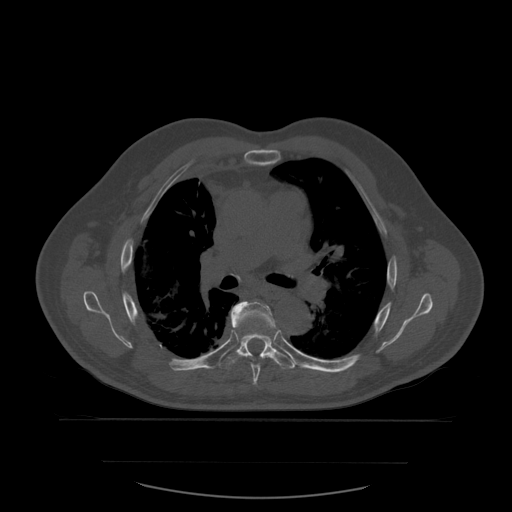
CT including the spine, one axial slice; slice 394 of 590 in the series (ordered by position); bone window (W 1800 / L 400 HU); 1.25 mm slice thickness; 512 × 512 image matrix, field of view 479 × 479 mm. Patient age 71 years. Case-level facts recorded for this patient, not image findings: primary cancer: lung.
Structures marked on this image (semi-automatic segmentation, software-assisted and operator-edited):
- T6 vertebra: box from (x=231, y=301) to (x=276, y=387) px
- T7 vertebra: (x=219, y=304)–(x=296, y=370)